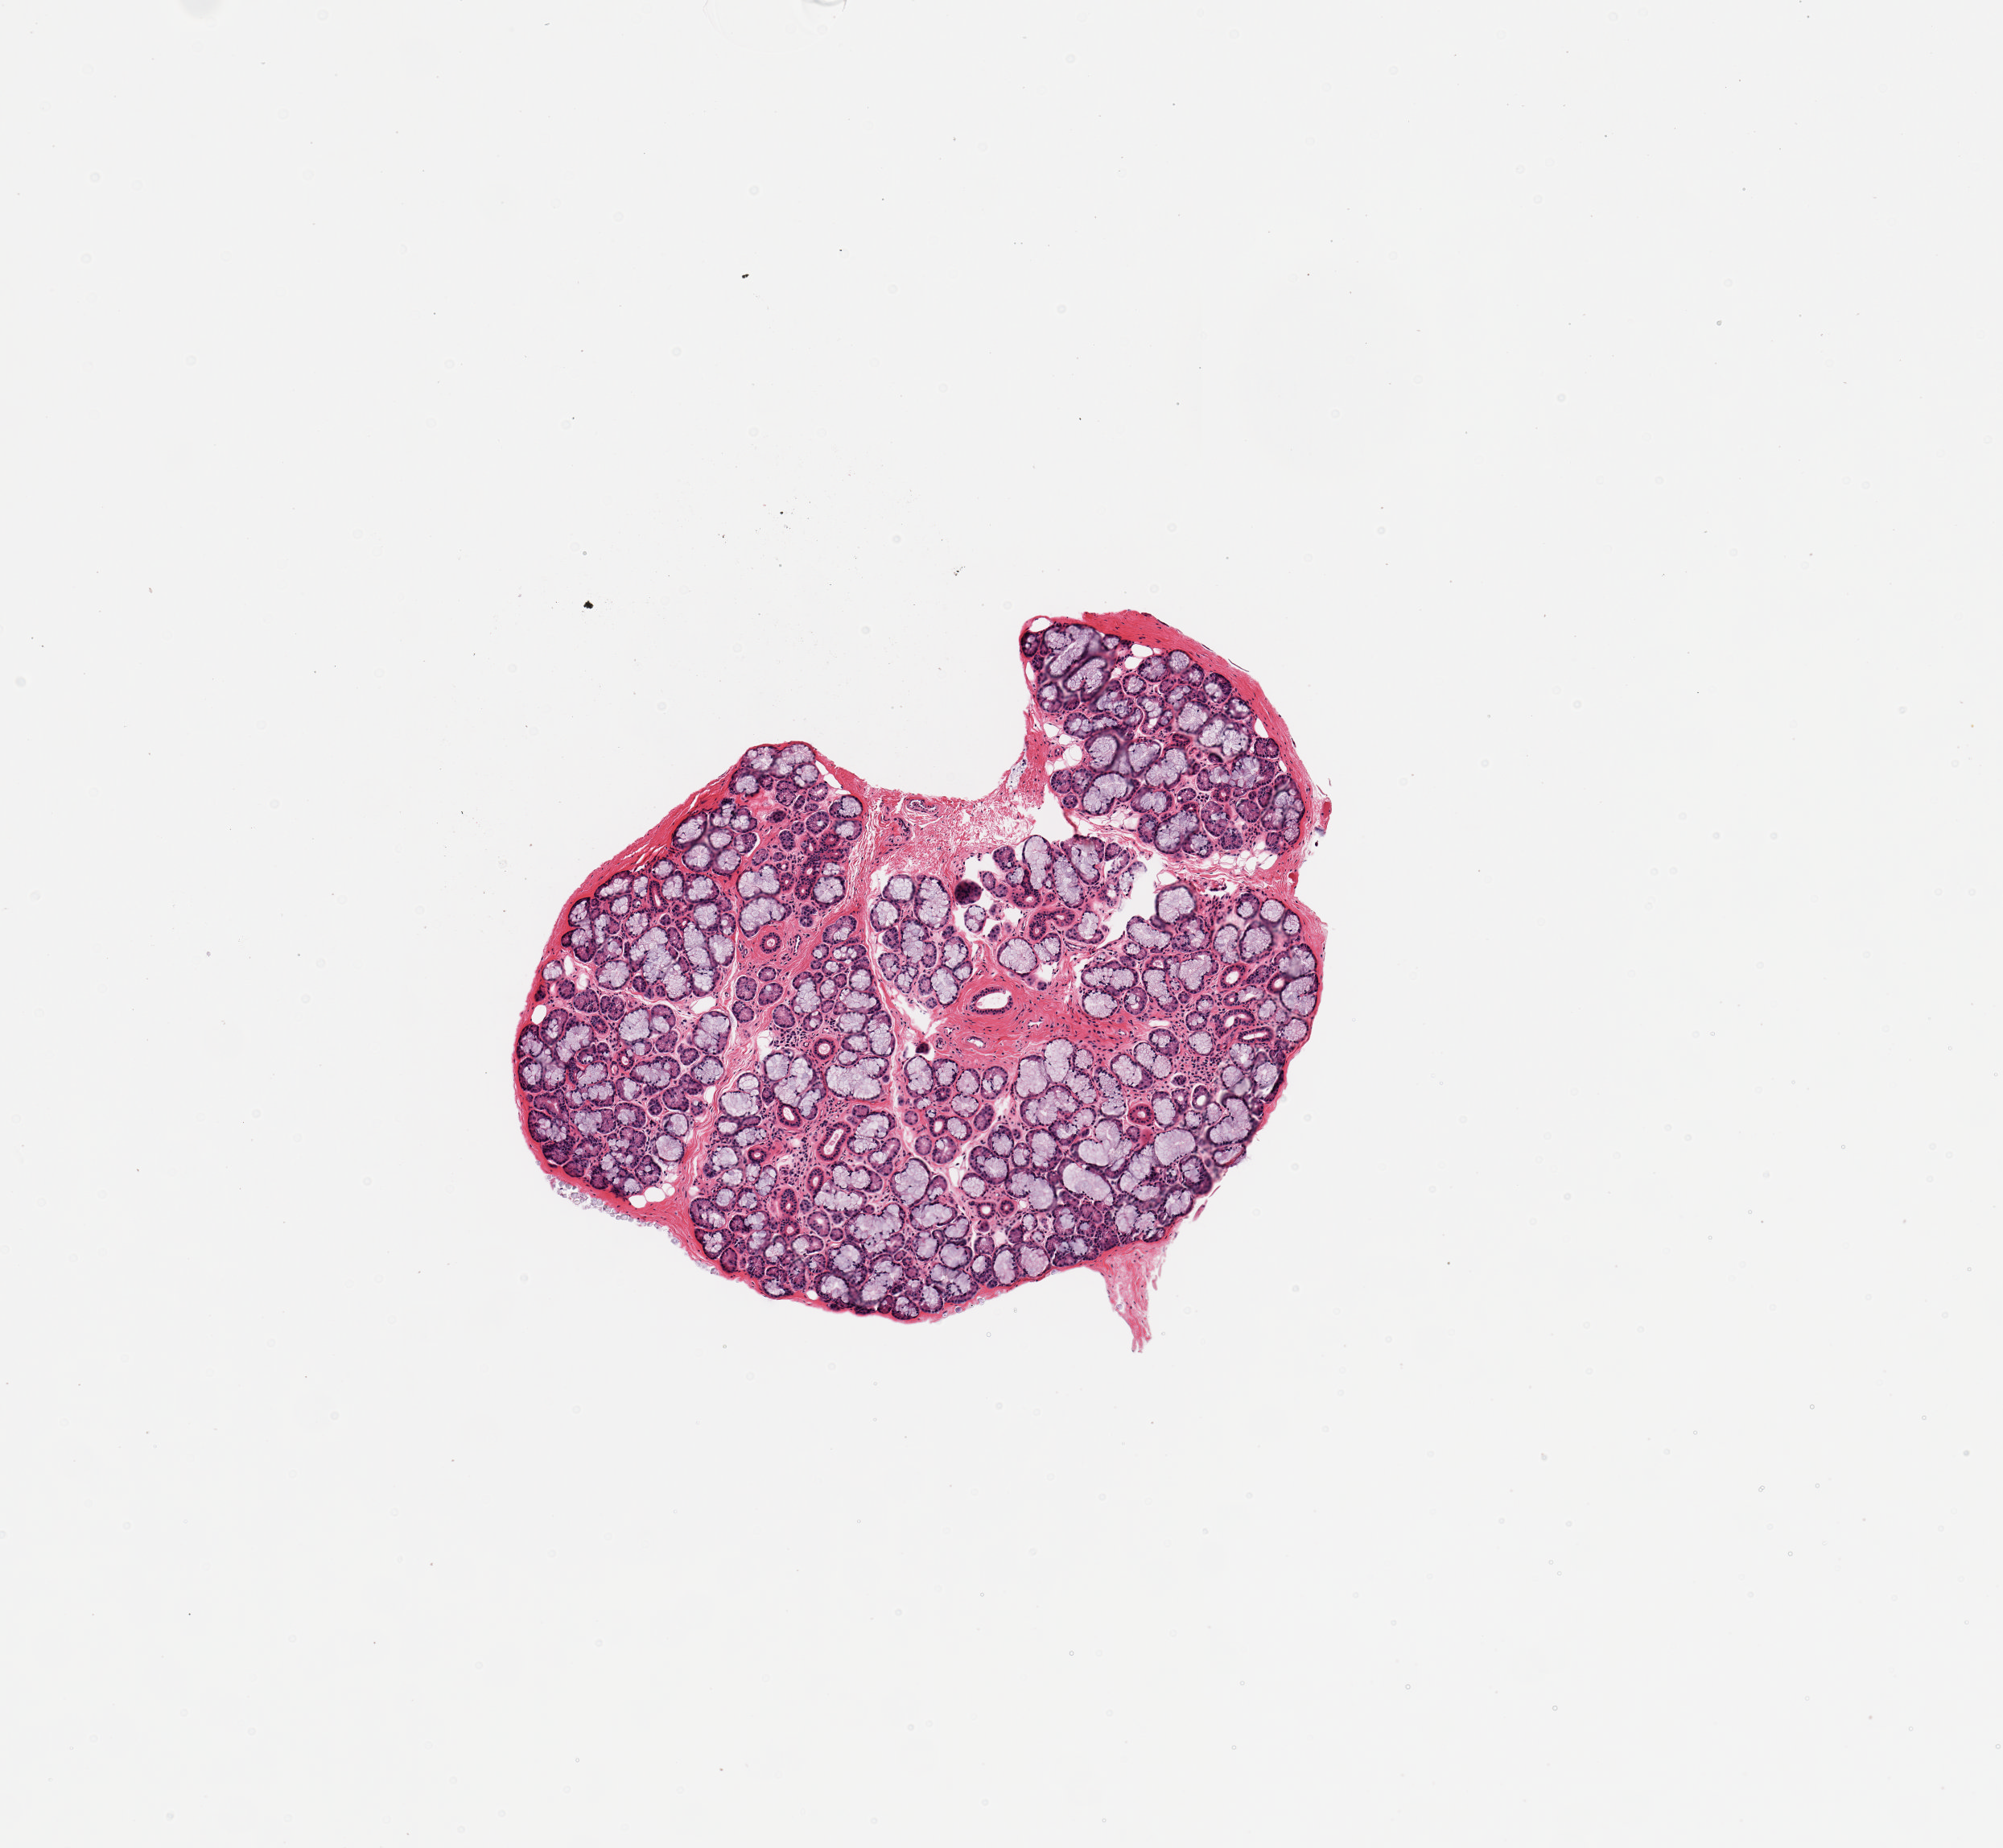
Whole-slide image, H&E stain, low-resolution overview of the scanned area, about 4.9 x 4.5 mm (slide scanned at 20x). PAXgene-fixed paraffin-embedded (PFPE) section. Target tissue: minor salivary gland. Tissue donor sample. Donor sex: female.
- pathologist's review note for this sample: 1 piece; well trimmed minor salivary gland